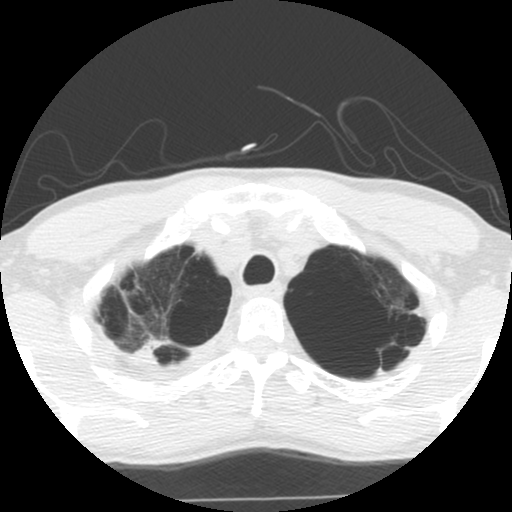
Low-dose screening chest CT, one axial slice; reconstruction kernel STANDARD; lung window (W 1500 / L -600 HU); 2.5 mm slice thickness; 512 × 512 image matrix, field of view 295 × 295 mm.
Outlined on this slice (outlined manually by an expert reader):
- lesion 1 (tumor, upper lobe of right lung): box from (x=132, y=338) to (x=165, y=360) px